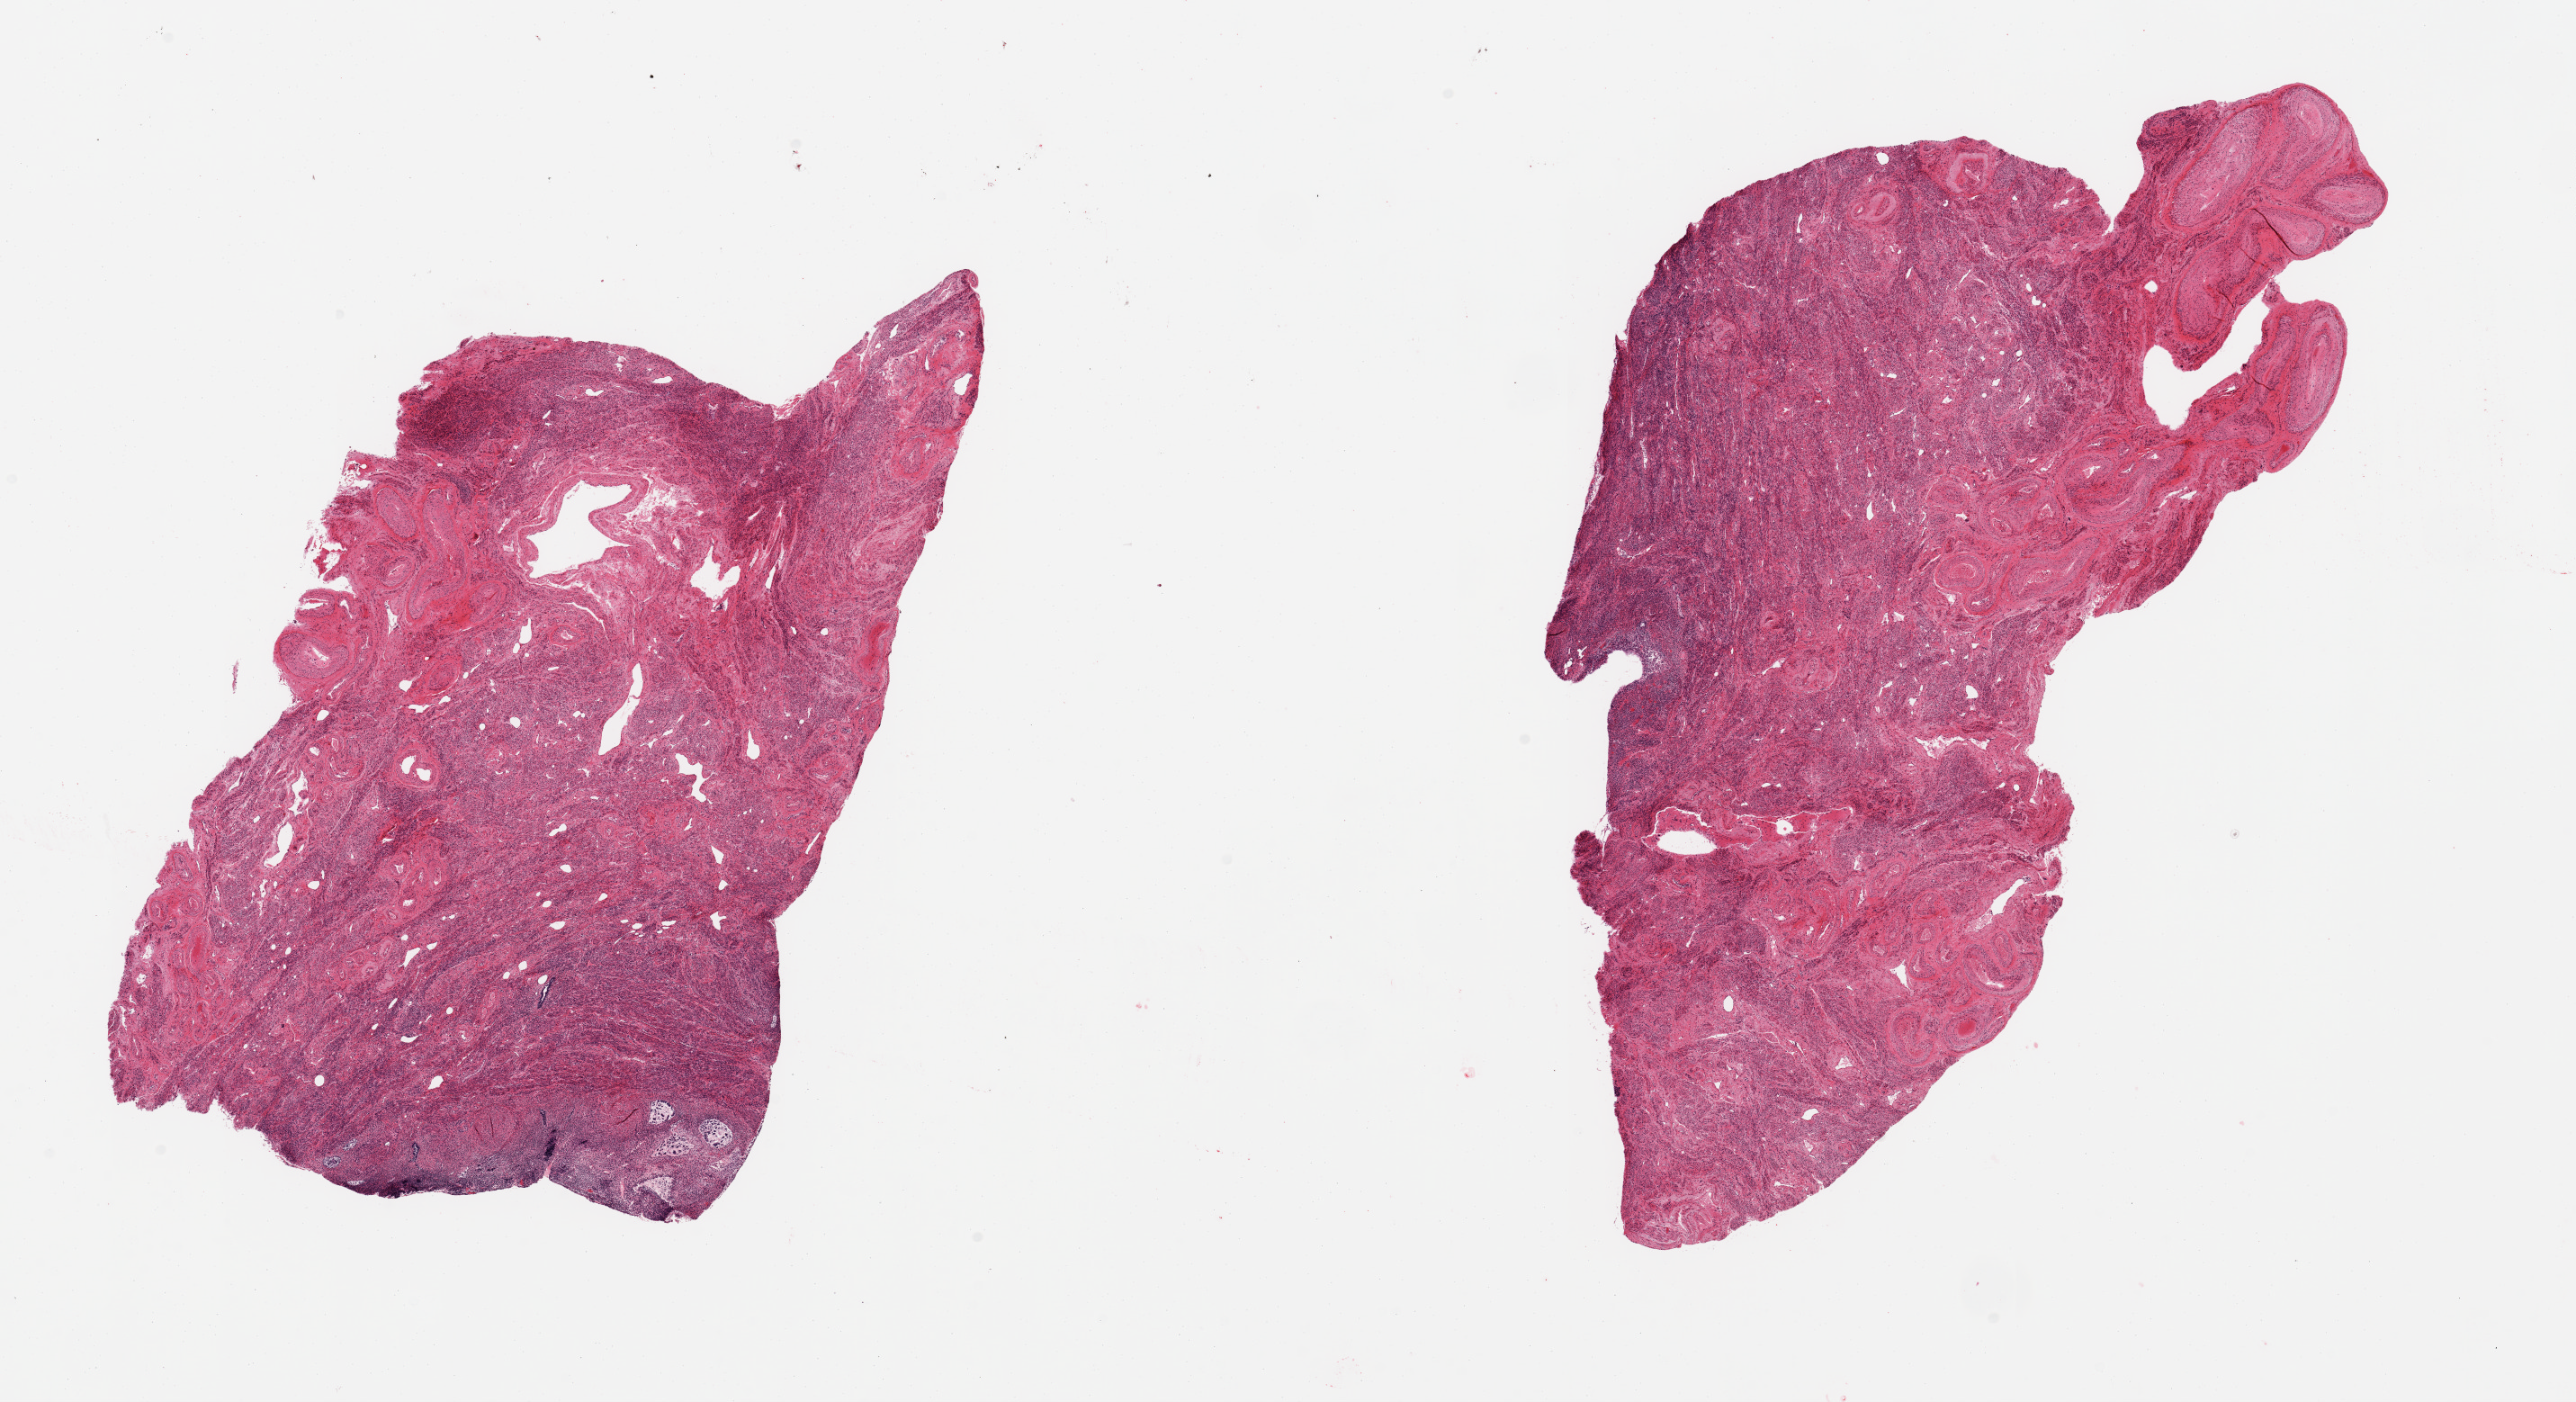
Digitized hematoxylin and eosin (H&E)-stained section, whole scanned area (about 22.6 x 12.3 mm, acquisition: 20x scan) shown as a low-resolution overview. PAXgene-fixed, paraffin-embedded tissue. Sampled site (target tissue): uterus. Donor tissue sample. Donor sex: female.
* review note (as recorded): 2 pieces; endometrium totally autolyzed; myometrium intact